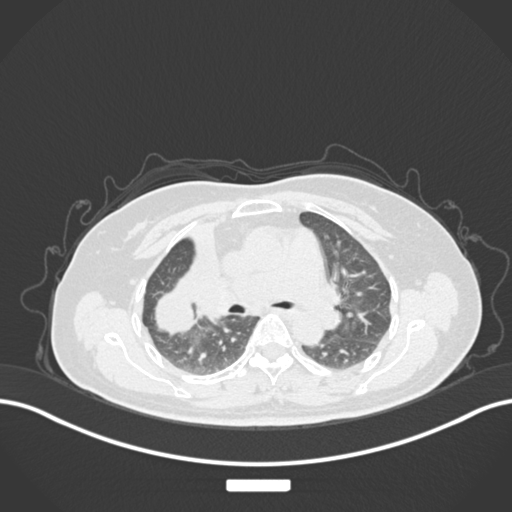
Chest CT, one axial slice. Position 95 of 177 along the scan axis. 120 kVp. Lung window (W 1500 / L -600 HU). 1 mm slice thickness. 512 × 512 image matrix, field of view 400 × 400 mm. Patient: female, 60 years. From the clinical record (not read from this slice): clinical TNM (as recorded): T3 N1 M1.
Outlined on this slice (bounding box drawn by a radiologist):
- lung tumour (recorded histology: adenocarcinoma): bounding box [x1, y1, x2, y2] px = [138, 272, 199, 342]